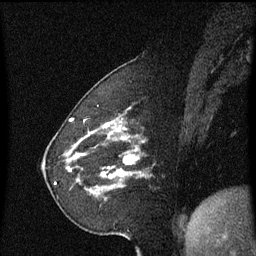
Breast MRI (dynamic contrast-enhanced), one sagittal slice; dynamic contrast-enhanced series, image 2 of 3 at this slice position (ordered by acquisition); 1.5 T; TE 4.2 ms, TR 8.4 ms; 2.2 mm slice thickness; 256 × 256 image matrix, field of view 200 × 200 mm. Female patient, age 60 years. From the clinical record (not read from this slice): setting: breast cancer imaged before/during neoadjuvant chemotherapy; receptor status: triple-negative.
Annotated regions visible in this slice (semi-automatic segmentation, software-assisted and operator-edited):
- analysis volume of interest (the breast-tissue region the enhancement analysis was run in; not a lesion): bounding box [x1, y1, x2, y2] px = [68, 142, 143, 201]
- tumour enhancement mask (voxels above the 70 % enhancement threshold inside the analysis volume of interest): [70, 156, 138, 179]